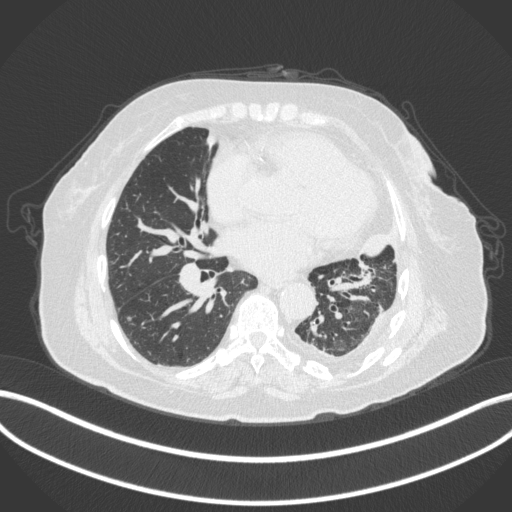
Chest CT, one axial slice; position 164 of 399 along the scan axis; 120 kVp; lung window (W 1500 / L -600 HU); 512 × 512 image matrix, field of view 400 × 400 mm. Patient: female, 75 years. Case-level facts recorded for this patient, not image findings: clinical TNM (as recorded): T3 N3 M1.
Annotated regions visible in this slice (rectangle marked by the reading radiologist):
- lung tumour (recorded histology: adenocarcinoma): bounding box (x1, y1, x2, y2) in pixels: (359, 228, 387, 259)